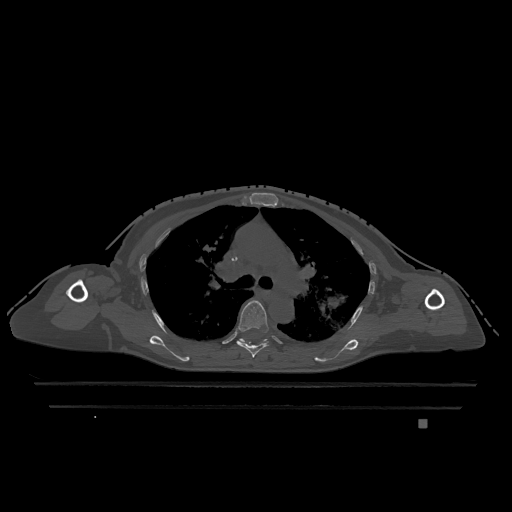
CT including the spine, one axial slice. Position 827 of 1317 along the scan axis. Bone window (W 1800 / L 400 HU). 0.5 mm slice thickness. 512 × 512 image matrix, field of view 500 × 500 mm. Patient: female, 74 years. From the clinical record (not read from this slice): primary cancer: lung.
Annotated regions visible in this slice (semi-automatically segmented with operator editing):
- T5 vertebra: bounding box (x1, y1, x2, y2) in pixels: (236, 300, 269, 358)
- T6 vertebra: (239, 338, 268, 344)